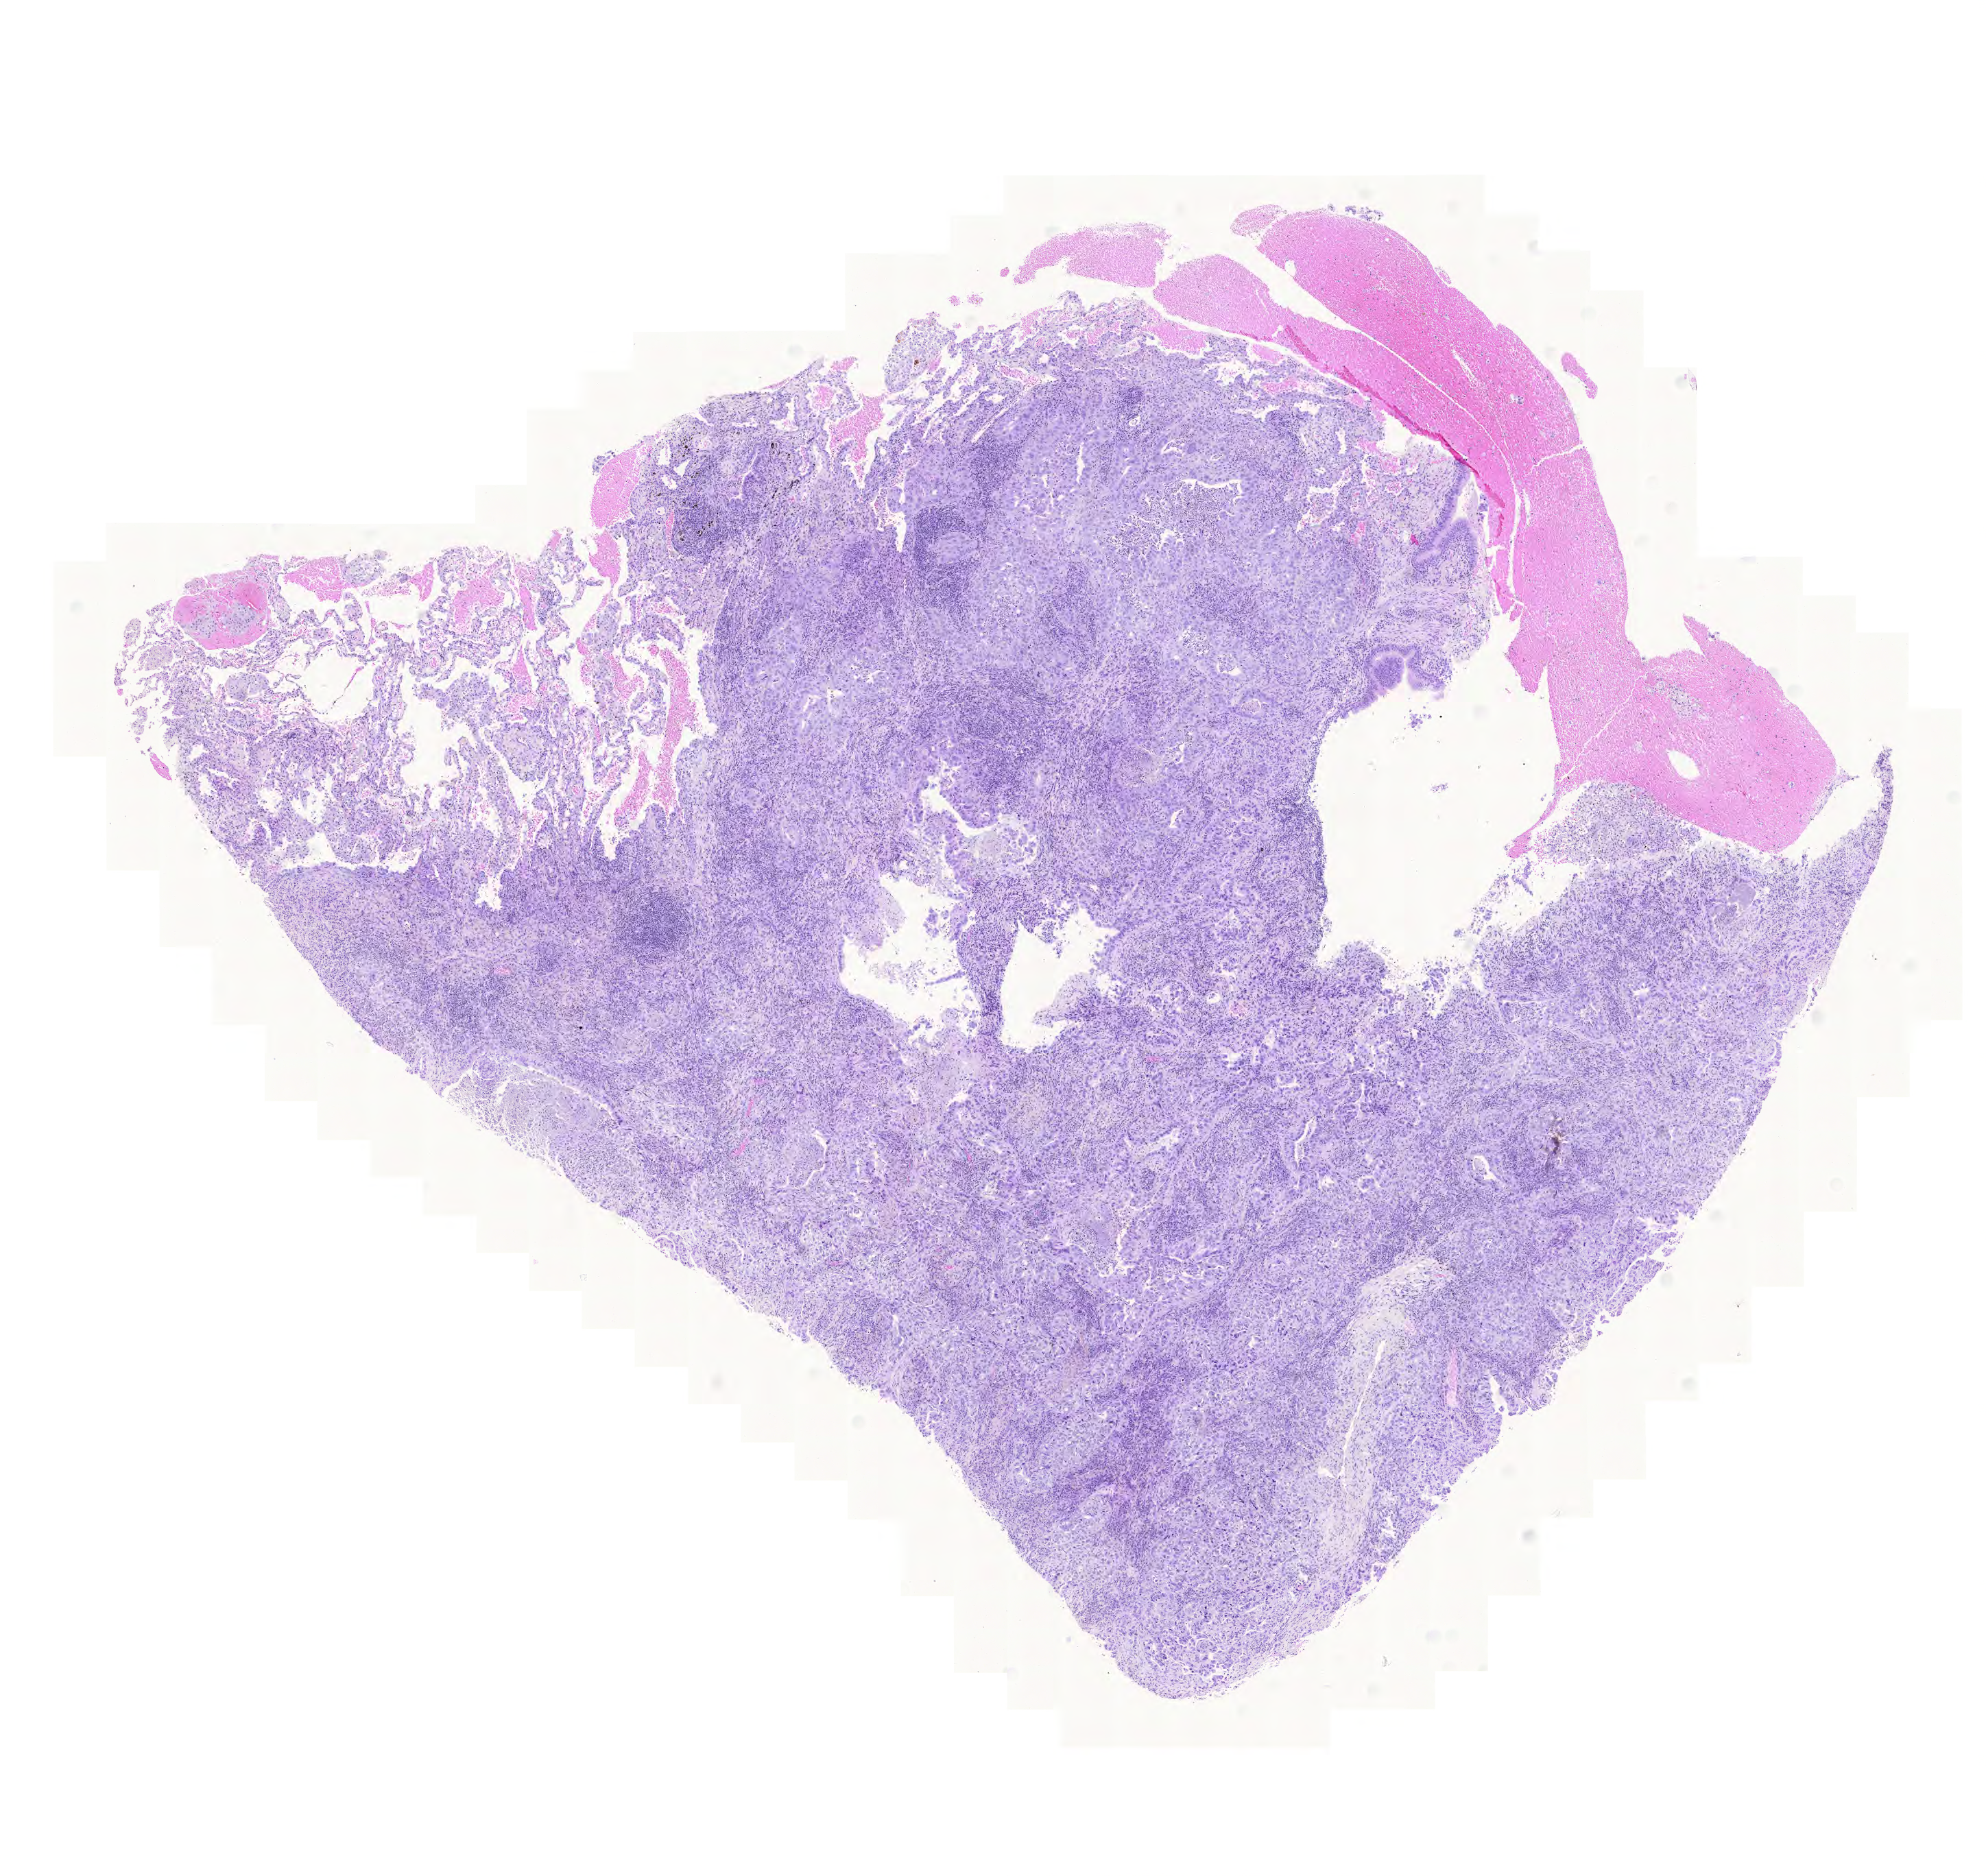
Hematoxylin and eosin (H&E) stained whole-slide image — a low-resolution overview of the entire scanned area, about 10.8 x 10.2 mm (slide scanned at 20x). Formalin-fixed paraffin-embedded (FFPE) diagnostic section. Sample: primary tumour, lung. Male patient; age at initial diagnosis 68 years.
AJCC pathologic stage: IB (6th edition). Diagnosis: Adenocarcinoma with mixed subtypes (upper lobe, lung). TNM: T2 N0 M0. Laterality: left.